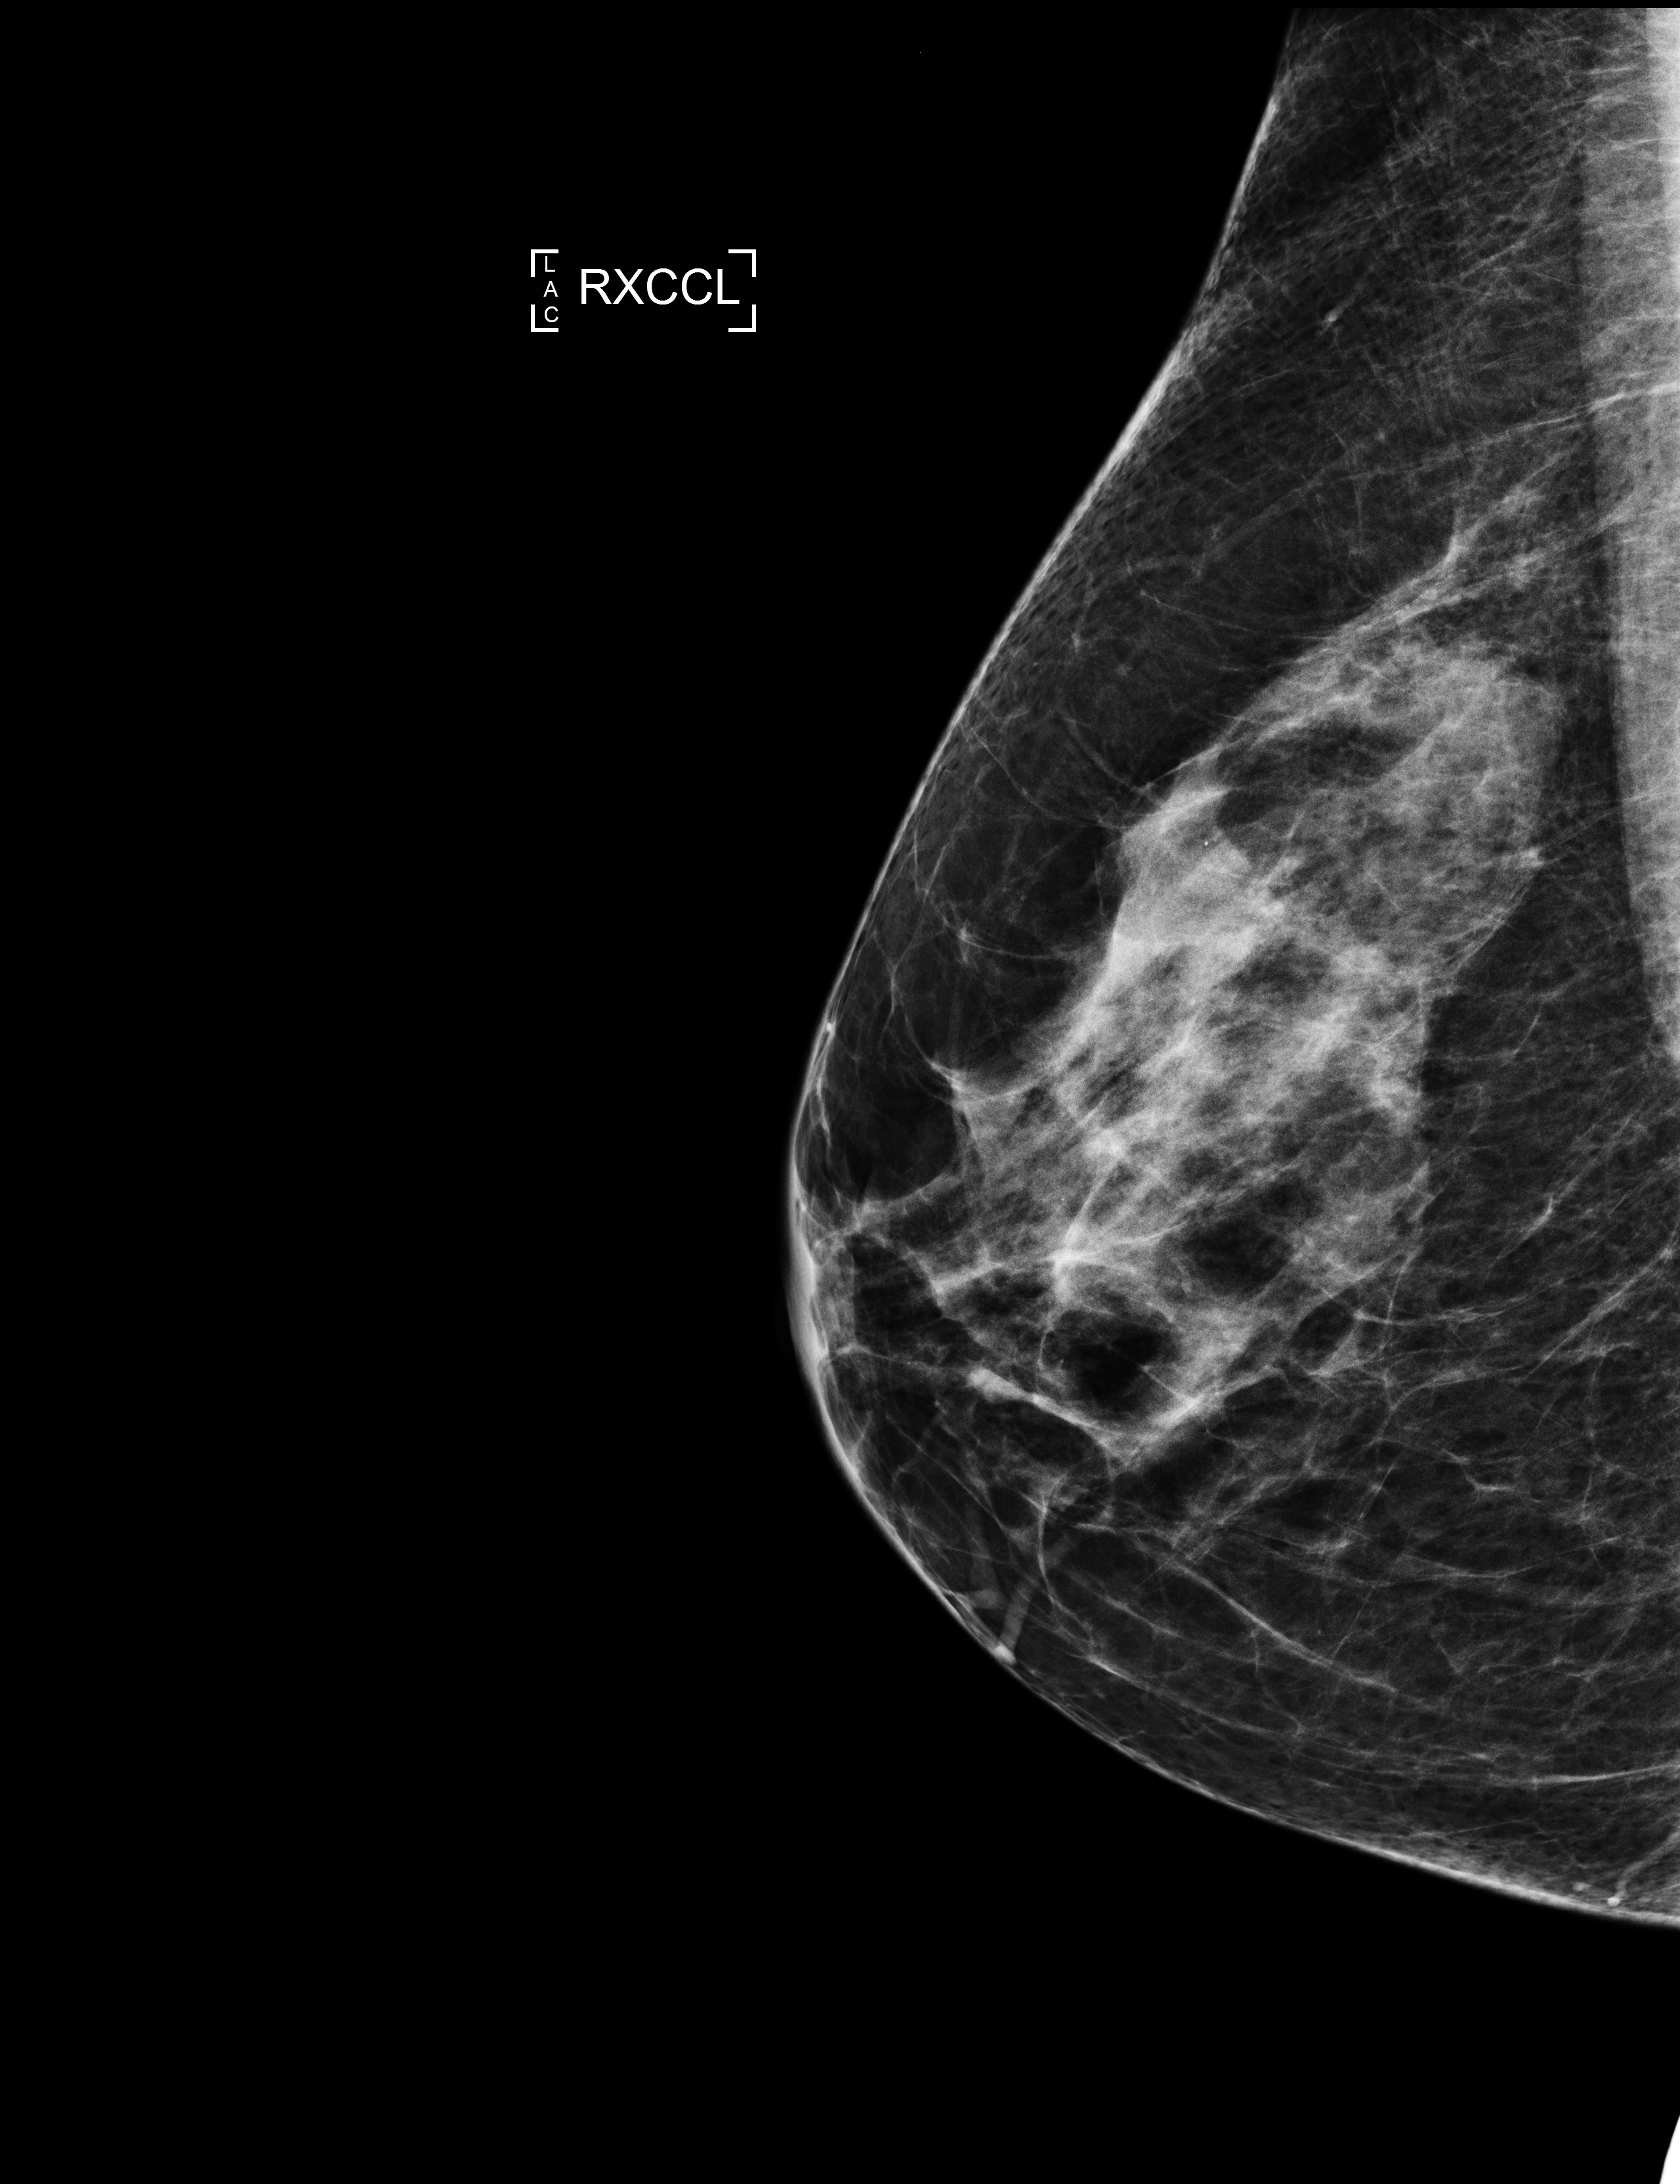
Full-field digital mammogram (FFDM), right breast, laterally exaggerated craniocaudal (XCCL) view, annual screening mammography examination. Patient: female, 63 years.
Breast density at the screening exam (both breasts): heterogeneously dense (BI-RADS density category c).